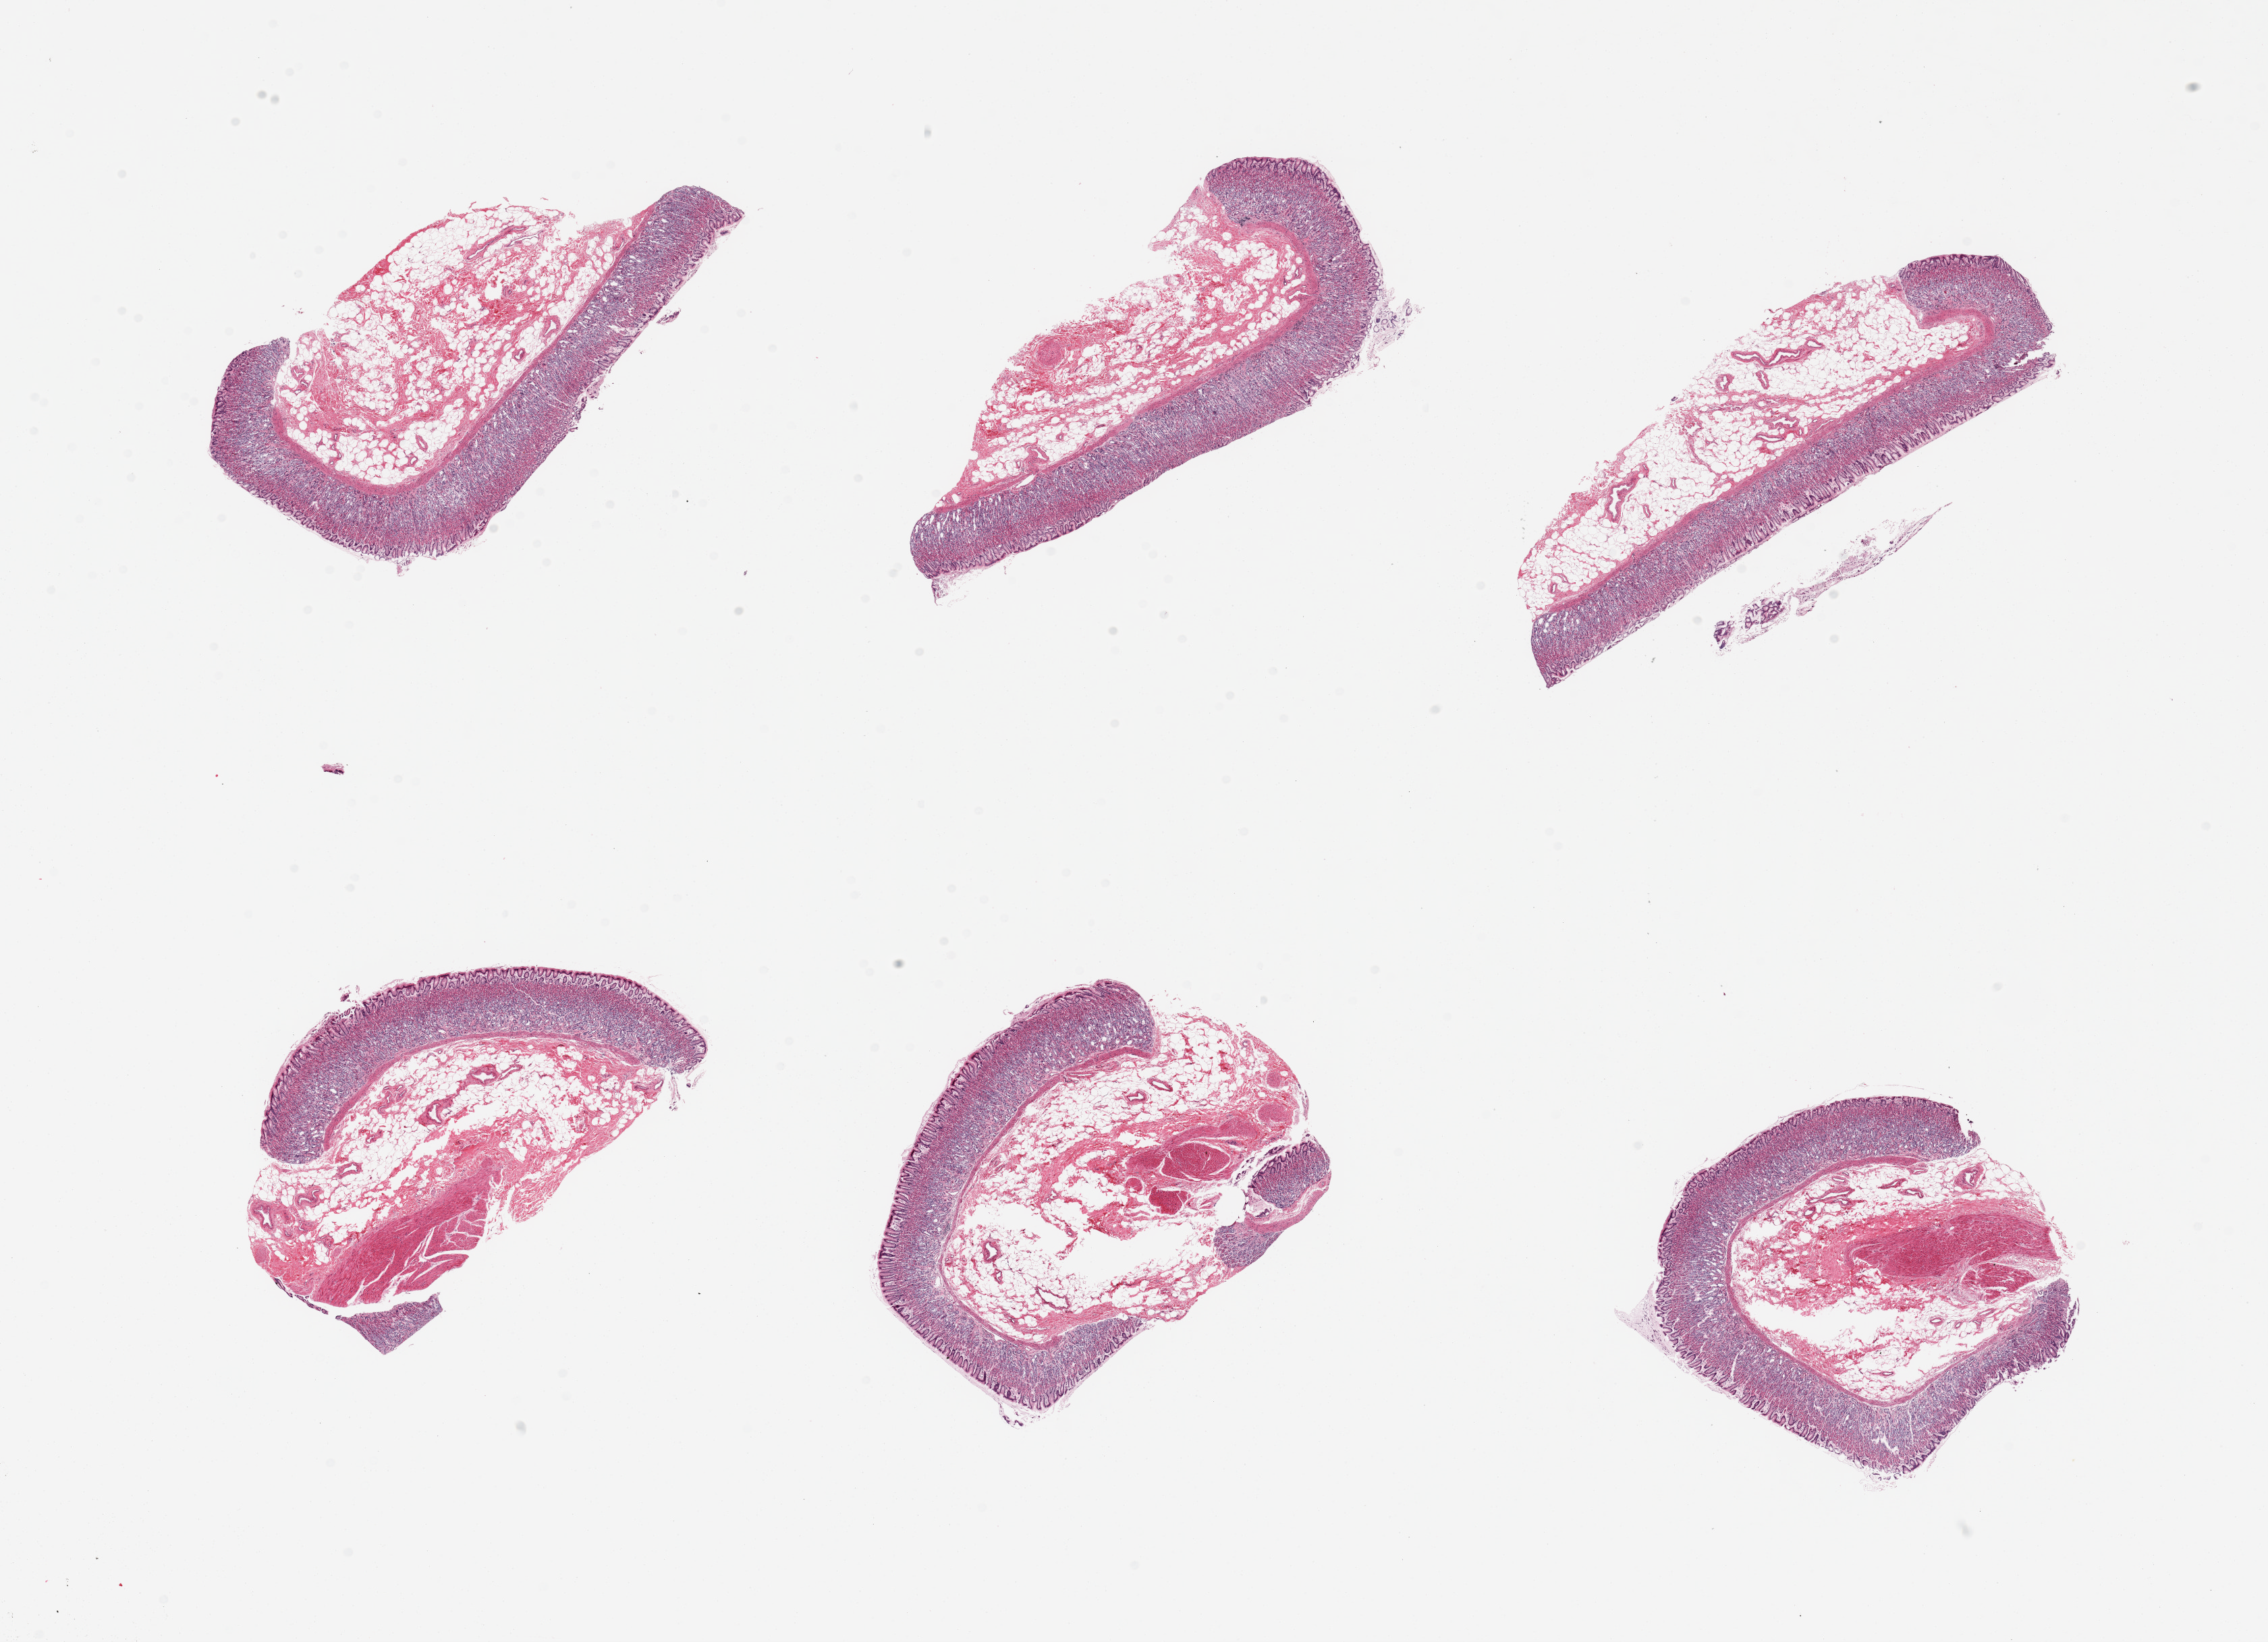
Whole-slide image, hematoxylin and eosin (H&E) stain, brightfield, whole scanned area (about 26.6 x 19.2 mm) shown as a low-resolution overview, PAXgene-fixed, paraffin-embedded tissue, sampled site (target tissue): stomach, tissue donor sample. Male donor.
Review note (as recorded): 6 pieces; all with mucosa, 3 with small amounts of muscularis propria.